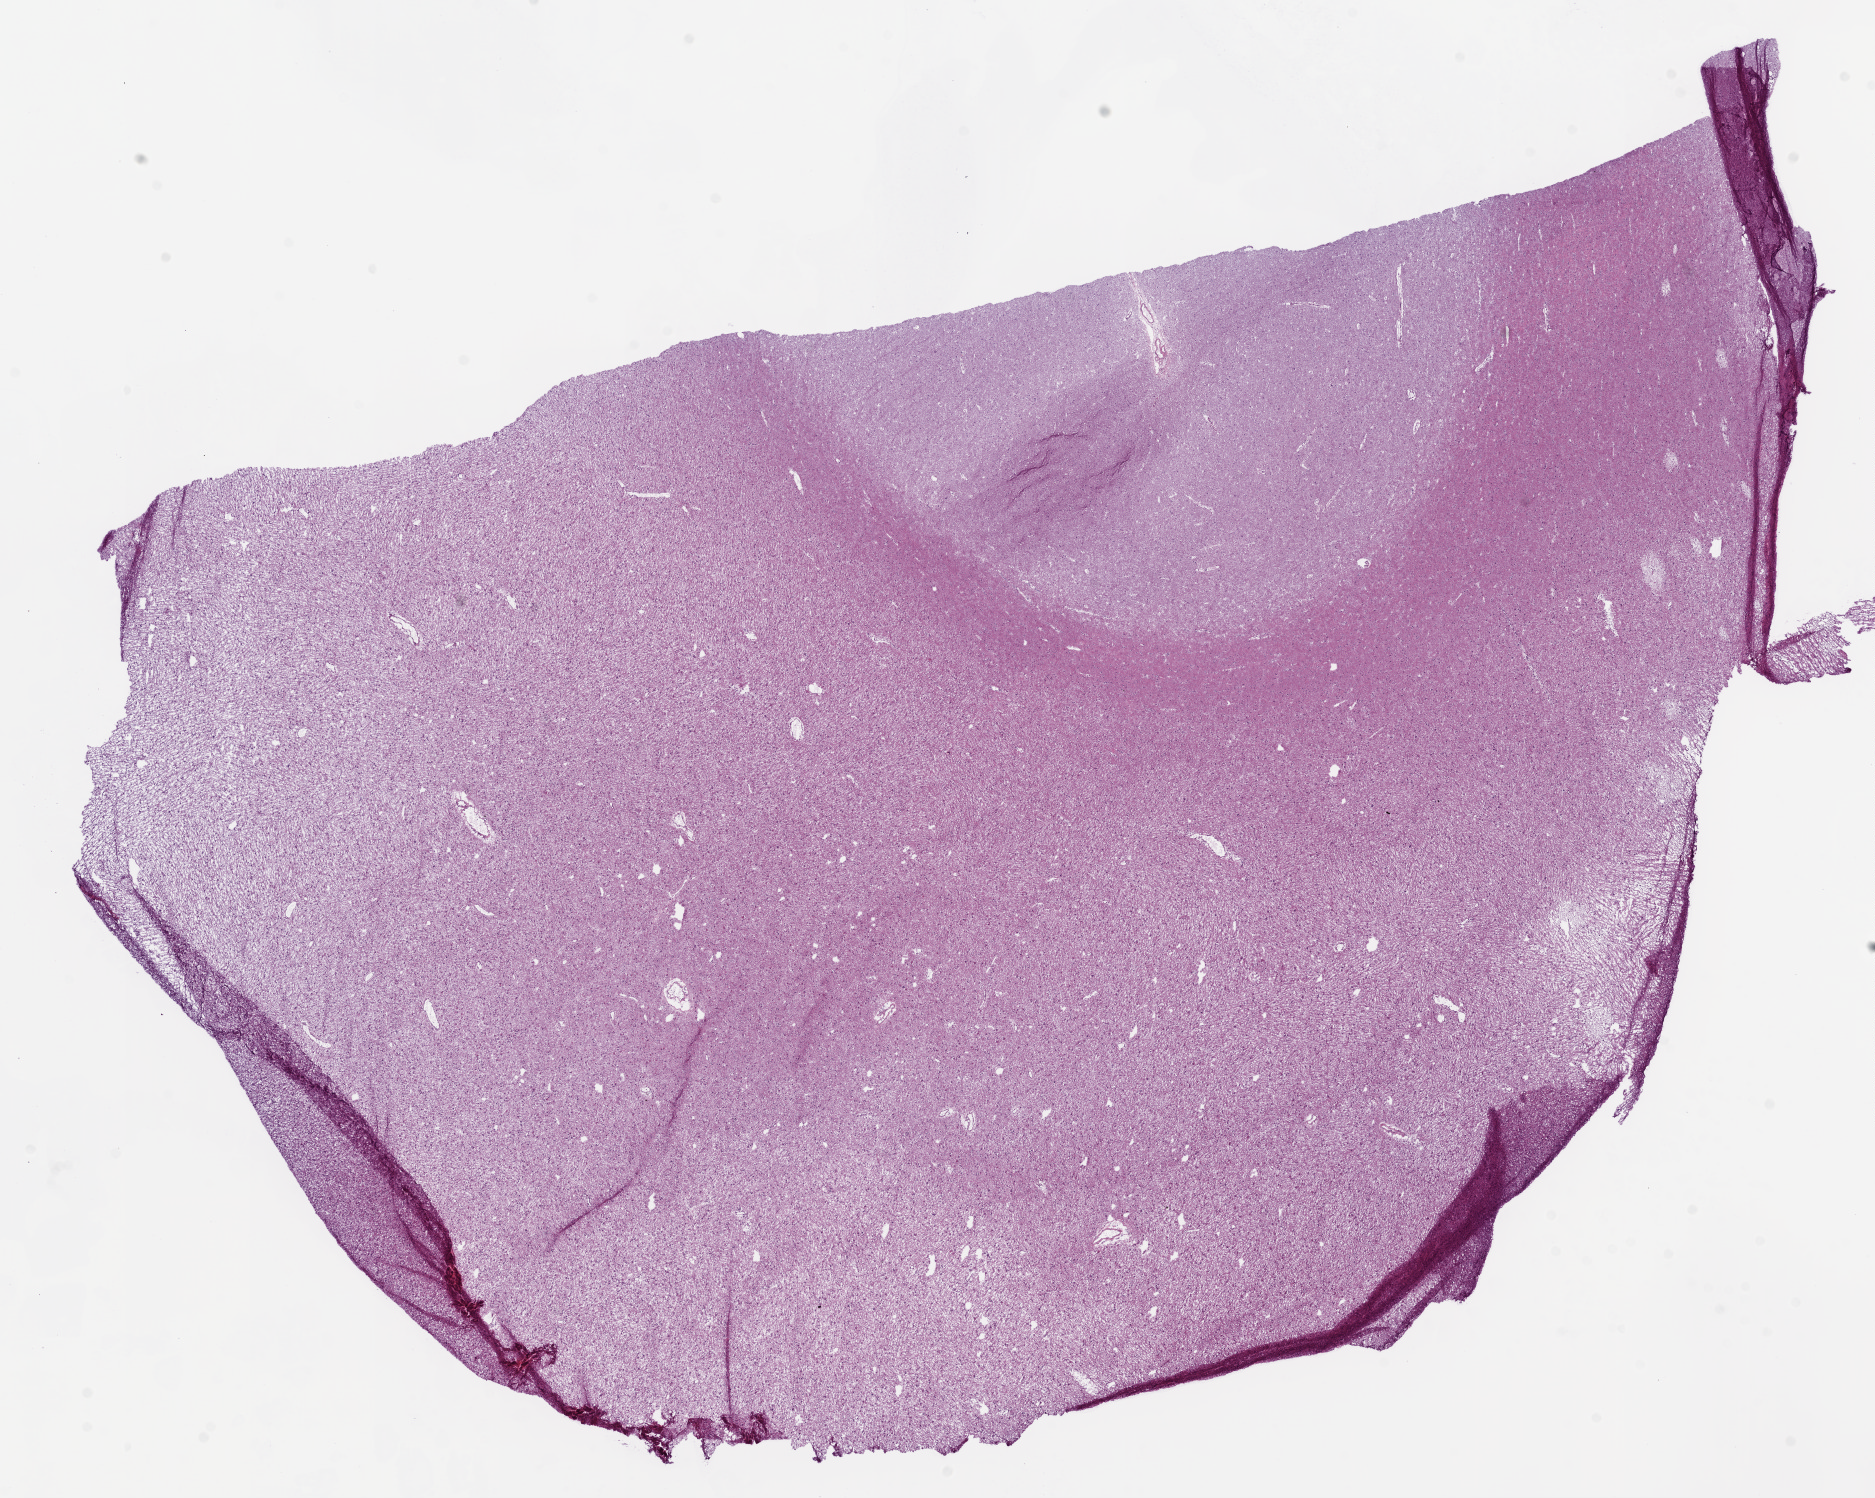
H&E whole-slide image, whole scanned area (about 15.0 x 12.0 mm, acquisition: 20x scan) shown as a low-resolution overview; frozen section; sample: primary tumour, brain. Male patient; age at initial diagnosis 32 years. Histologic grade: G3 (poorly differentiated). Slide review estimates, as recorded: tumour cells 100%, tumour nuclei 60%, normal cells 0%, stromal cells 0%, necrosis 0%.
Diagnosis: Mixed glioma (cerebrum).